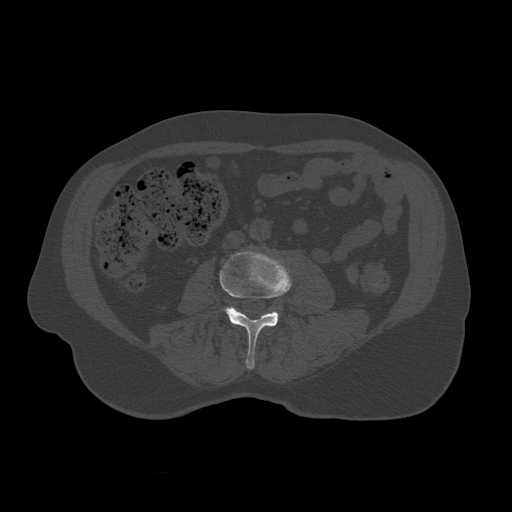
CT including the spine, one axial slice; slice 298 of 450 in the series (ordered by position); reconstruction kernel STANDARD; 120 kVp; bone window (W 1800 / L 400 HU); 1.25 mm slice thickness; 512 × 512 image matrix. Patient age 75 years. Case-level facts recorded for this patient, not image findings: primary cancer: prostate.
Outlined on this slice (semi-automatic segmentation, software-assisted and operator-edited):
- L3 vertebra: bounding box (x1, y1, x2, y2) in pixels: (220, 250, 293, 370)
- L4 vertebra: (278, 307, 280, 309)